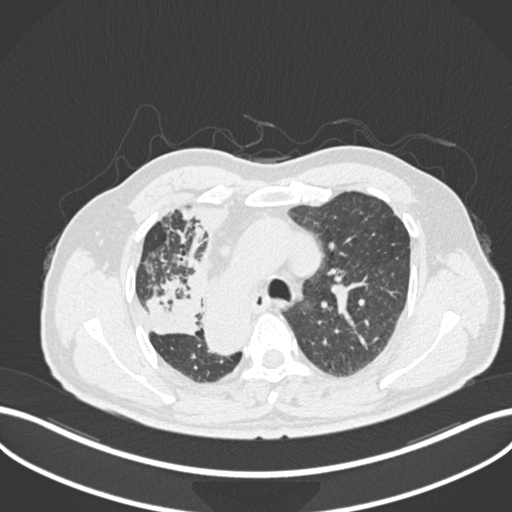
Chest CT, one axial slice; position 169 of 206 along the scan axis; reconstruction kernel B30f; lung window (W 1500 / L -600 HU); 1 mm slice thickness; 512 × 512 image matrix, field of view 400 × 400 mm. Male patient, age 67 years. From the clinical record (not read from this slice): clinical TNM (as recorded): T2a N0 M0.
Structures marked on this image (rectangle marked by the reading radiologist):
- lung tumour (recorded histology: squamous cell carcinoma): bounding box (x1, y1, x2, y2) in pixels: (143, 273, 200, 338)